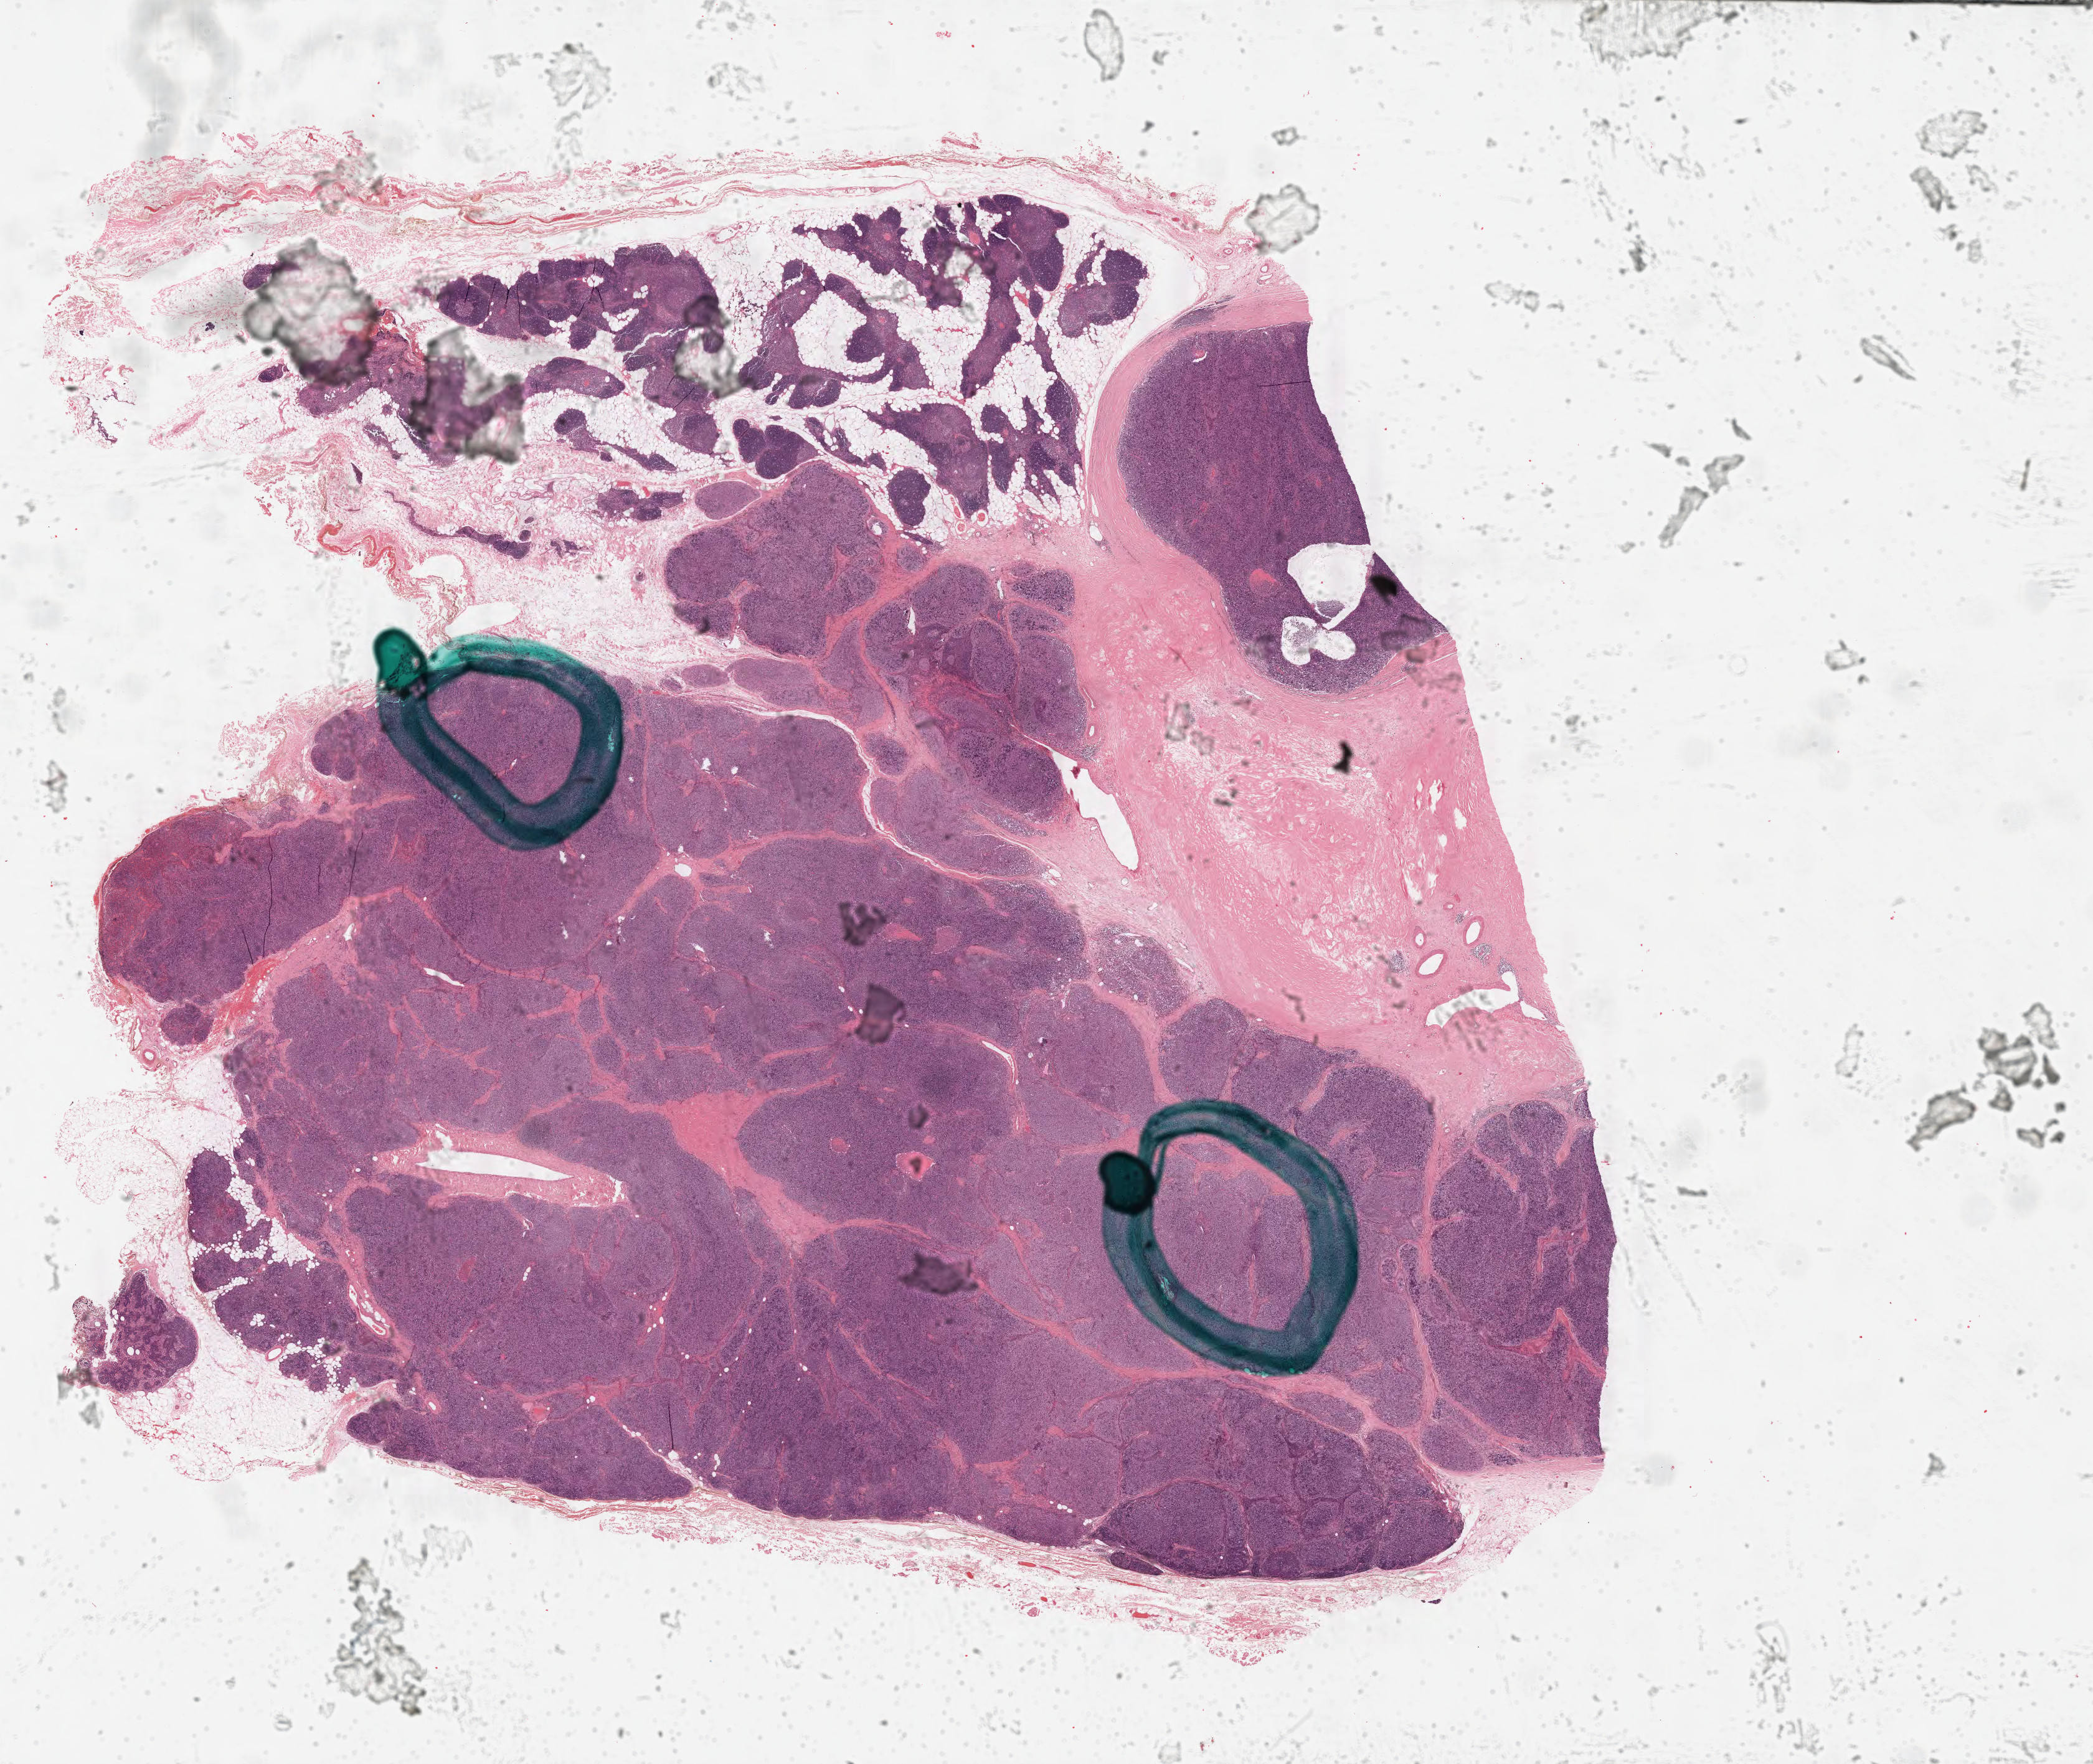
H&E-stained whole-slide image, a low-resolution overview of the entire scanned area, about 26.5 x 22.4 mm (acquisition: 40x scan), FFPE section, sample: primary tumour, thymus. Male patient; age at initial diagnosis 43 years.
Diagnosis: Thymoma, type B2, malignant.